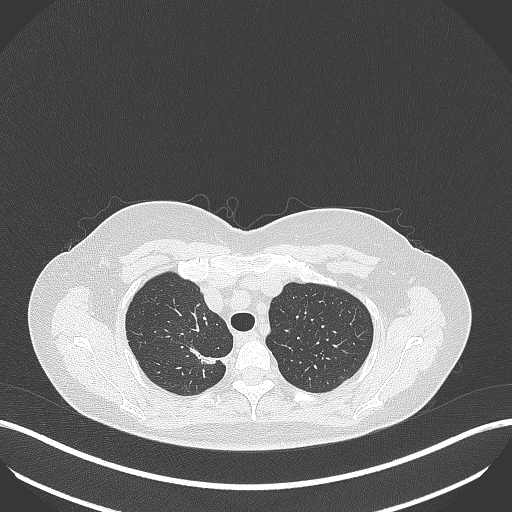
Chest CT, one axial slice. Slice 320 of 386 in the series (ordered by position). Reconstruction kernel B70f. Lung window (W 1500 / L -600 HU). 1 mm slice thickness. 512 × 512 image matrix, field of view 400 × 400 mm. Patient: female, 65 years. Case-level facts recorded for this patient, not image findings: clinical TNM (as recorded): T1b N0 M0; histopathological grade: G2.
Structures marked on this image (bounding box drawn by a radiologist):
- lung tumour (recorded histology: adenocarcinoma): box from (x=177, y=340) to (x=228, y=371) px